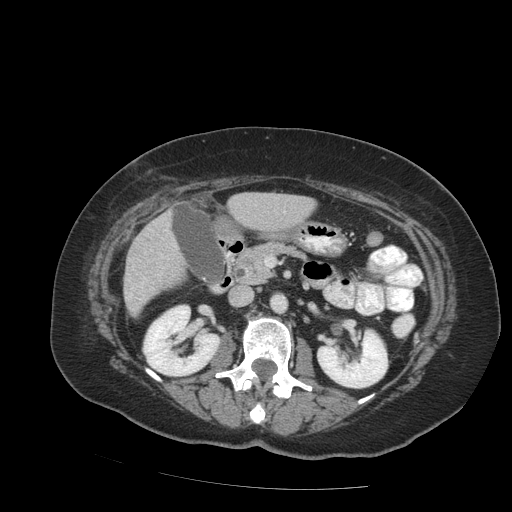
Contrast-enhanced abdominal CT (liver protocol), one axial slice. Position 33 of 99 along the scan axis. 140 kVp. Soft-tissue window (W 400 / L 40 HU). 2.5 mm slice thickness. 512 × 512 image matrix, field of view 400 × 400 mm. Case-level facts recorded for this patient, not image findings: diagnosis: hepatocellular carcinoma (patient treated with transarterial chemoembolisation; whether this scan precedes or follows treatment is not stated here); TNM stage (as recorded): Stage-IVB; Child-Pugh class: A; tumour differentiation: moderately differentiated.
Structures marked on this image (semi-automatic segmentation, software-assisted and operator-edited):
- liver parenchyma outside the tumour (the mass and vessels are separate outlines, so this box may not span the whole liver): bounding box [x1, y1, x2, y2] px = [124, 192, 312, 316]